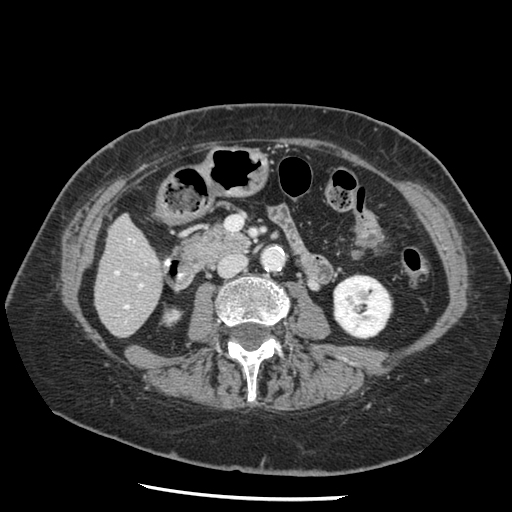
Contrast-enhanced abdominal CT, one axial slice; slice 39 of 148 in the series (ordered by position); reconstruction kernel STANDARD; soft-tissue window (W 400 / L 40 HU); 512 × 512 image matrix, field of view 330 × 330 mm. Female patient, age 85 years. Case-level facts recorded for this patient, not image findings: diagnosis: colorectal cancer liver metastases, imaged before liver resection; multiple liver metastases: no; largest metastasis: 0.9 cm; disease in both lobes: no.
Structures marked on this image (expert manual segmentation):
- hepatic veins: bounding box [x1, y1, x2, y2] px = [115, 271, 128, 308]
- liver: [96, 217, 163, 336]
- planned liver remnant (the part of the liver to remain after resection): [96, 217, 163, 333]